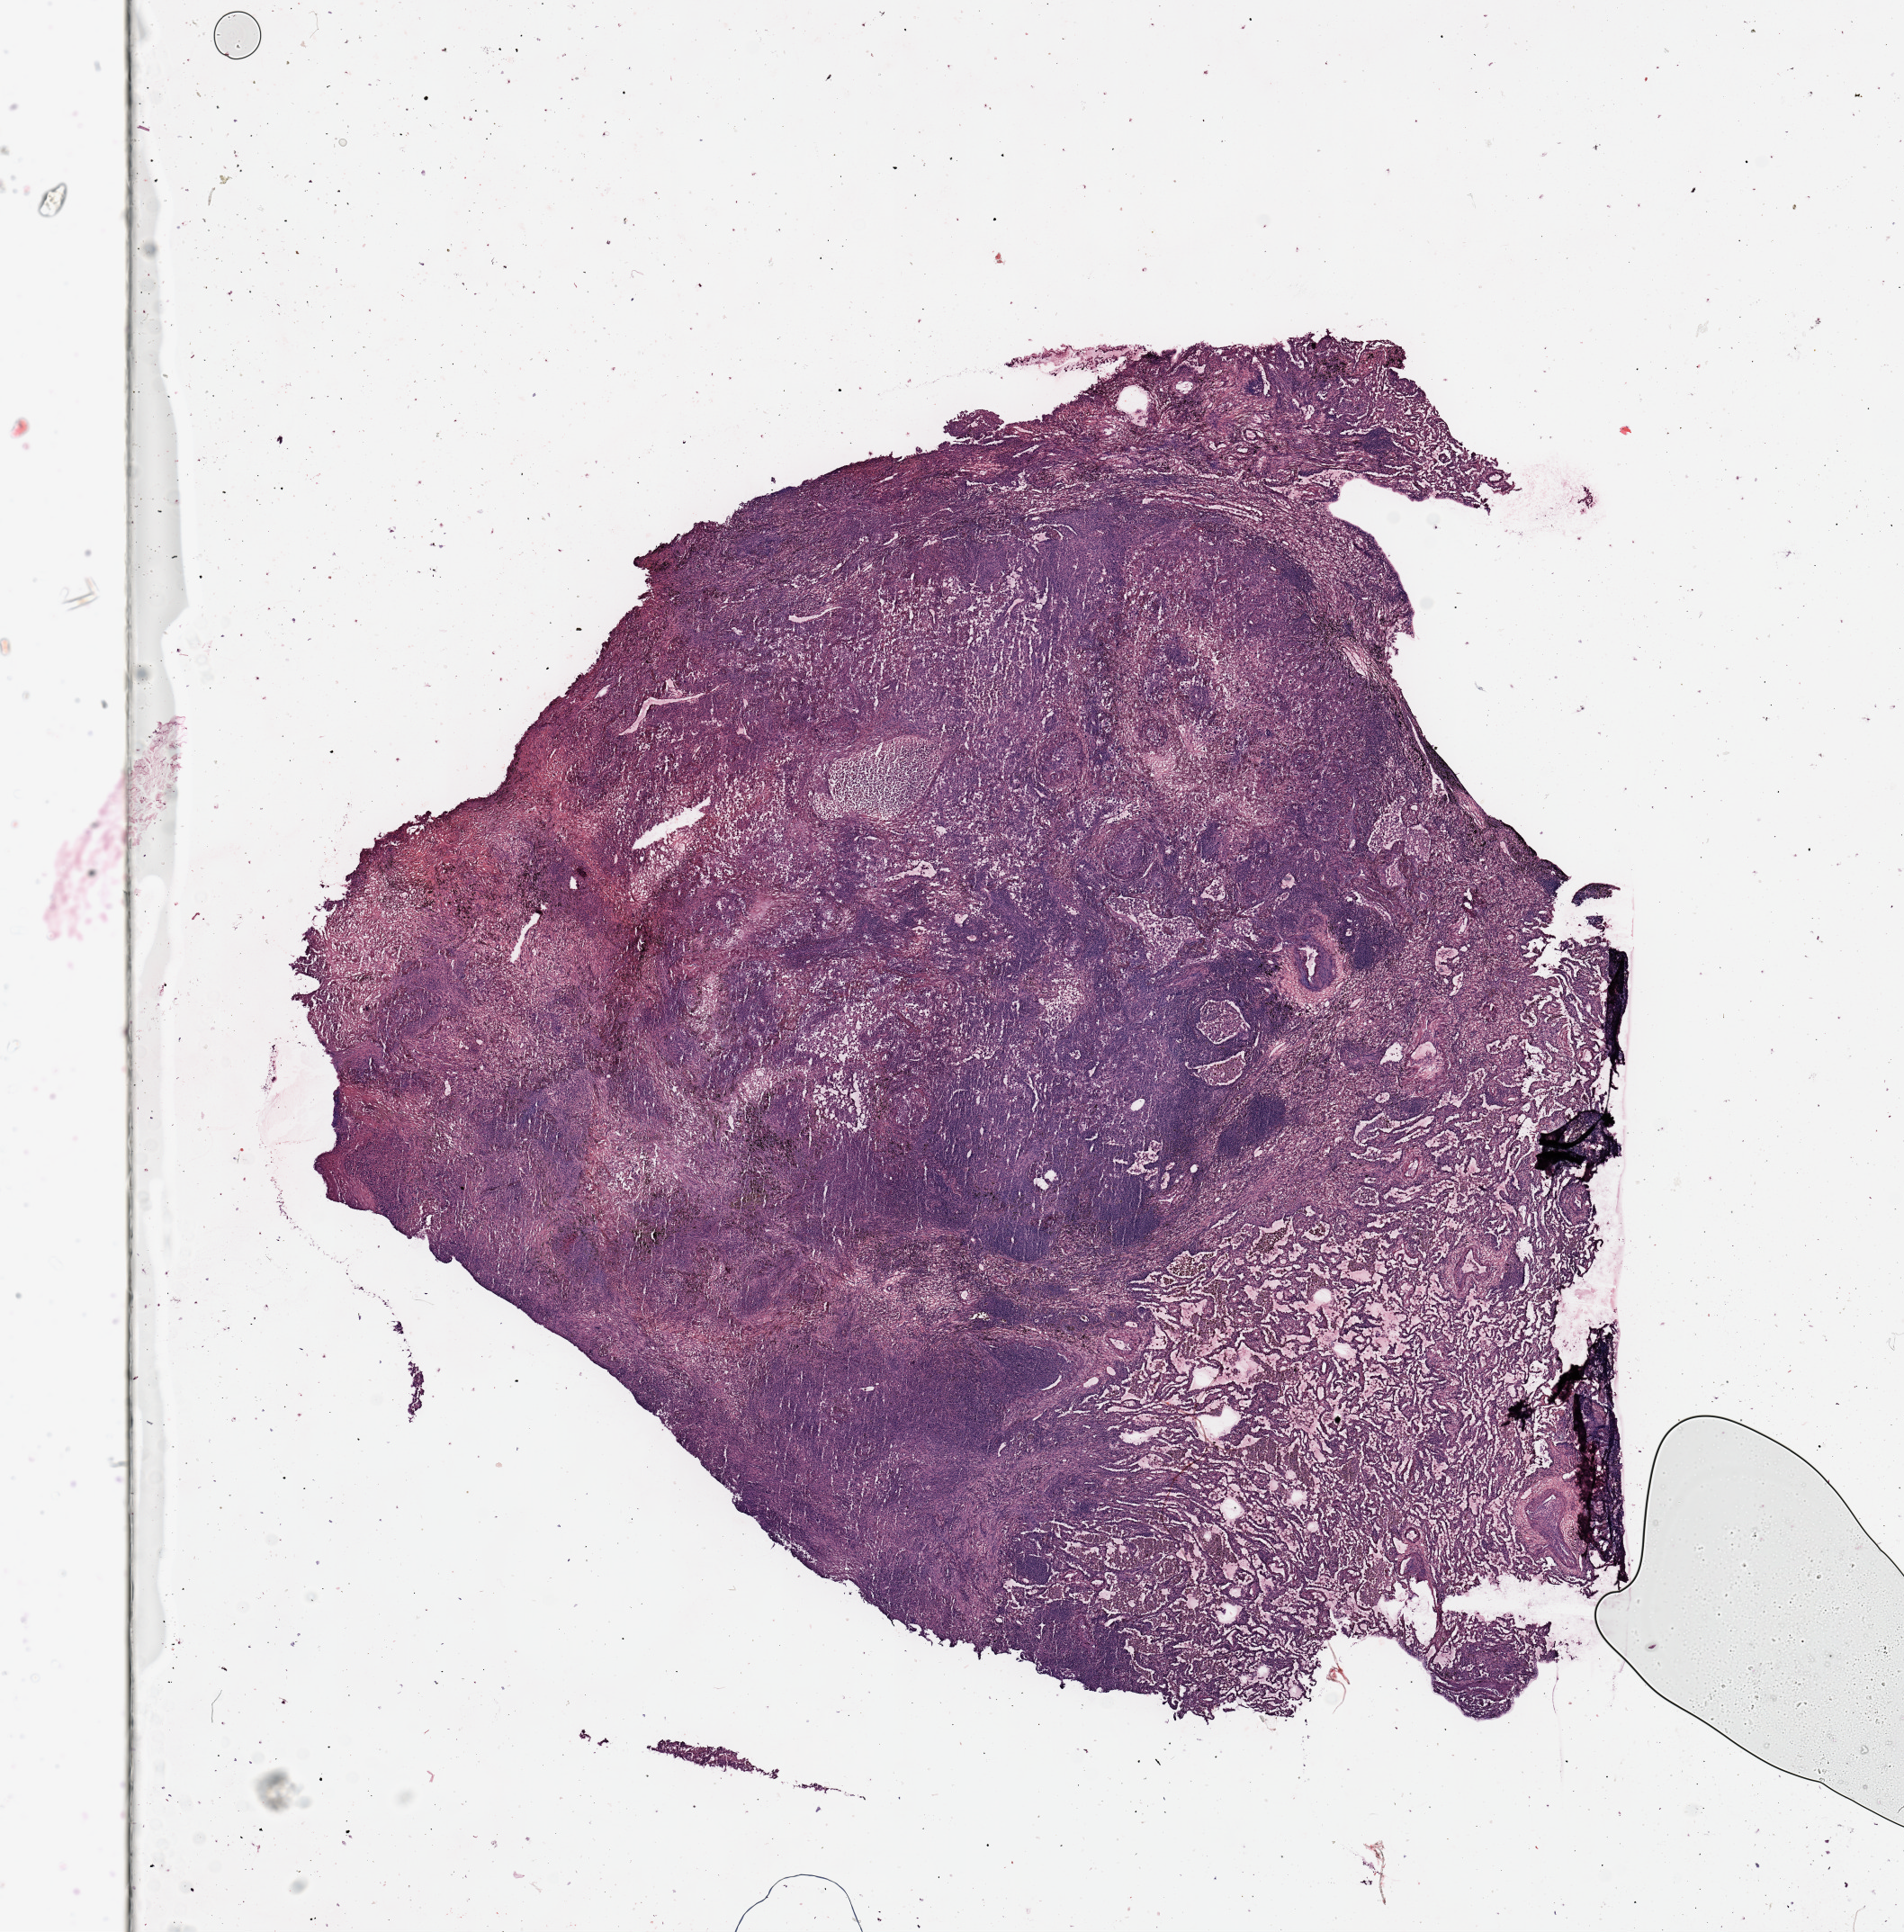
Hematoxylin and eosin (H&E) stained whole-slide image — a low-resolution overview of the entire scanned area, about 16.7 x 17.0 mm. Tumour tissue sample, lung. Male, 57 y/o. Histologic grade: G3 (poorly differentiated).
- histologic diagnosis: Adenocarcinoma, NOS
- AJCC pathologic stage: IB
- primary tumour site (as recorded): right upper lobe